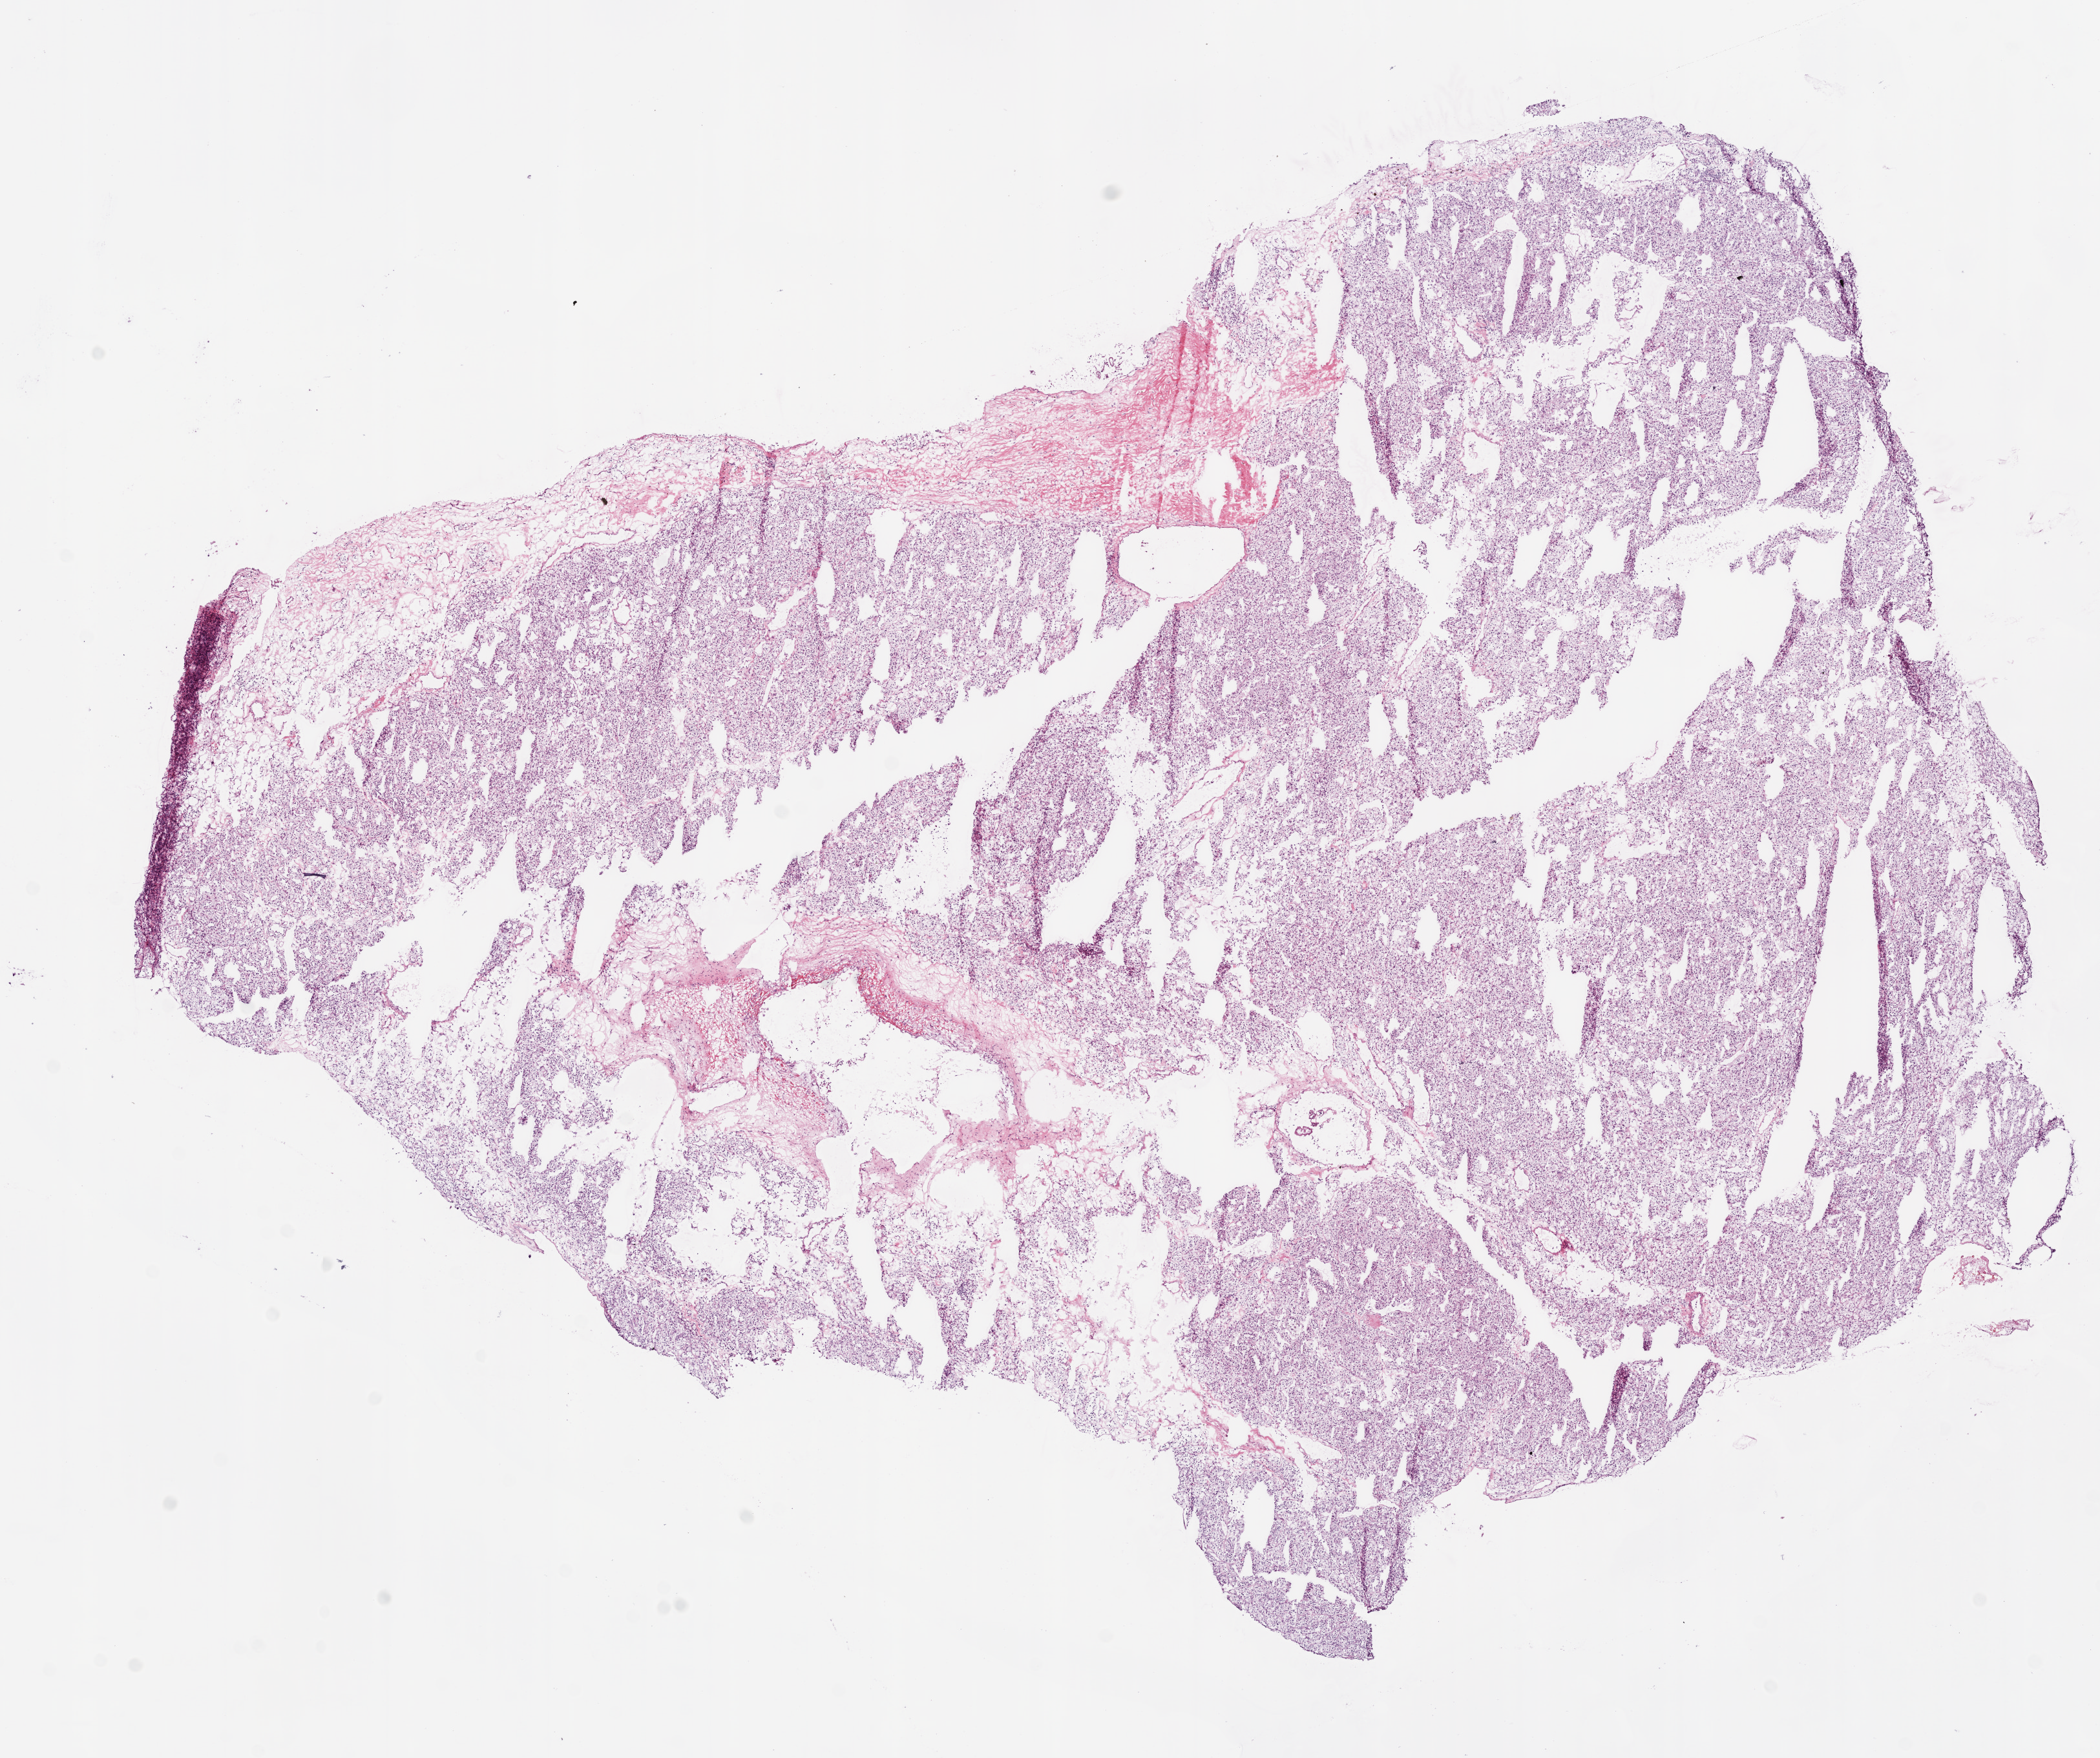
Digitized H&E tissue section (whole slide) — low-resolution overview of the scanned area, about 13.0 x 10.9 mm (acquisition: 20x scan), frozen section, kidney, primary tumour sample. Male patient; age at initial diagnosis 68 years. Histologic grade: G3 (poorly differentiated). Pathologist review of this section (percent, as recorded): tumour cells 85%, tumour nuclei 85%, normal cells 0%, stromal cells 15%, necrosis 0%.
Lymph nodes positive (case pathology): 0 of 5 examined. Diagnosis: Clear cell adenocarcinoma, NOS. AJCC pathologic stage: I.